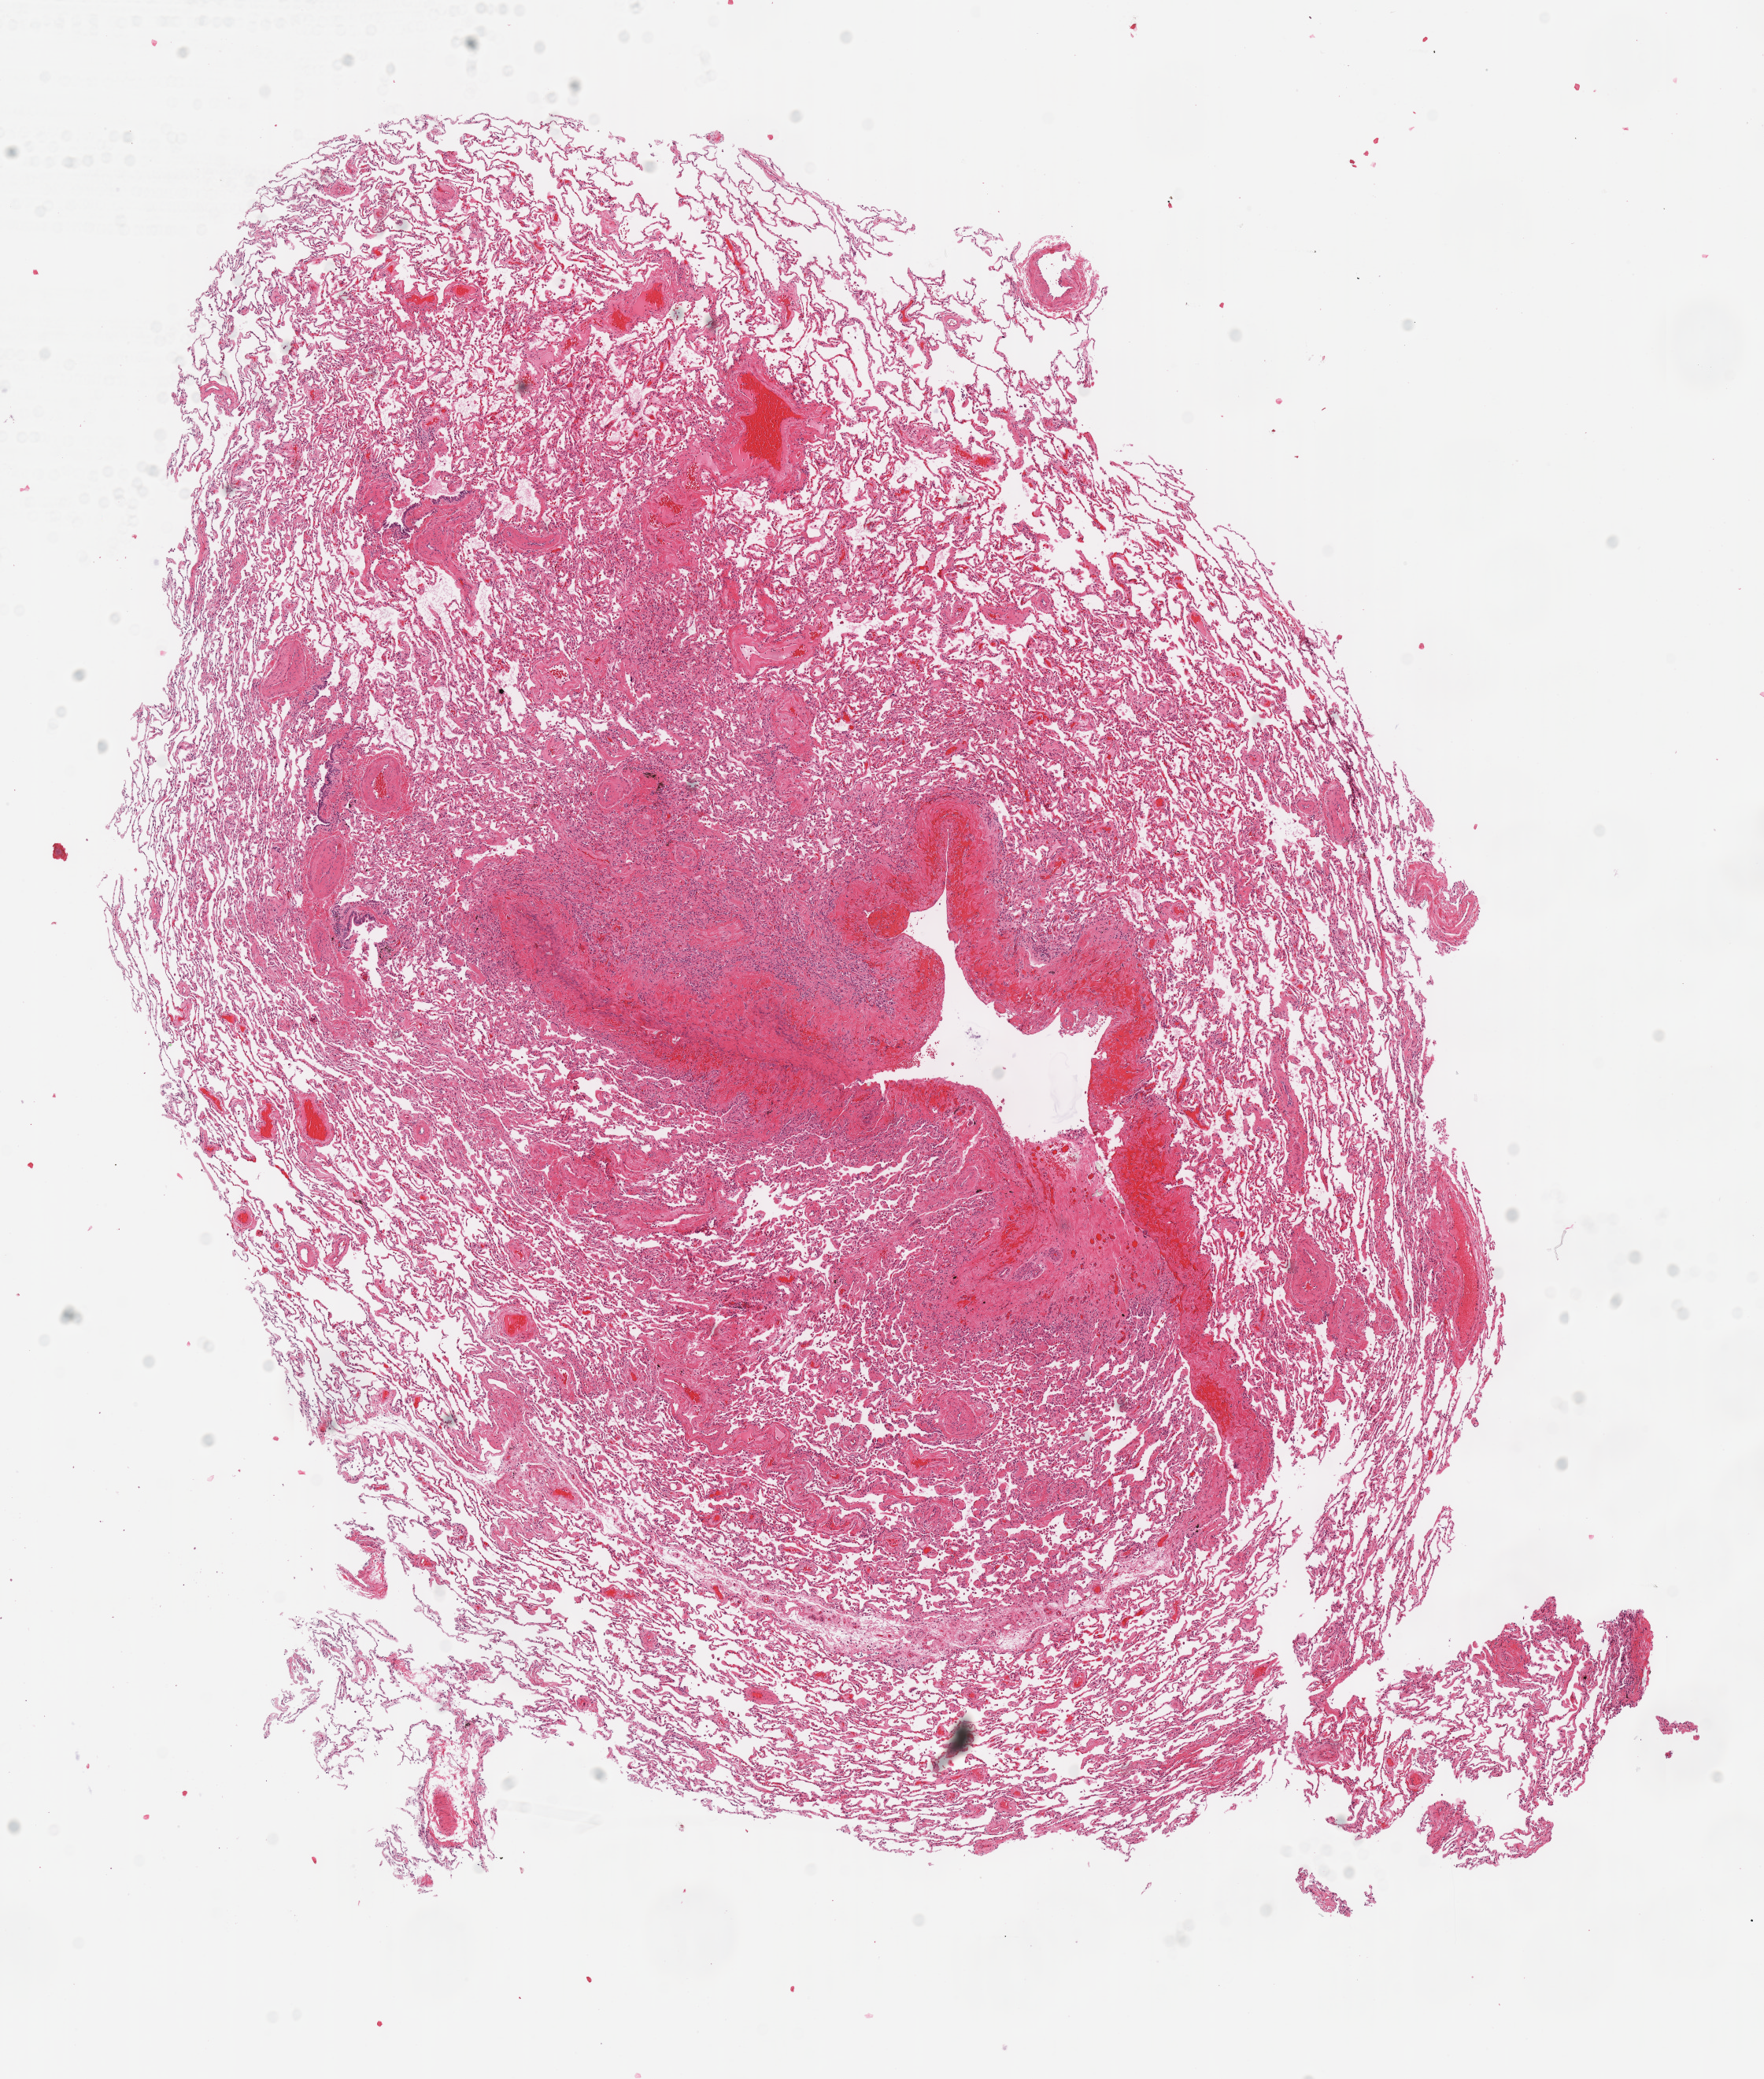
Hematoxylin and eosin (H&E) stained whole-slide image, shown as a low-resolution overview of the whole scanned area (about 8.8 x 10.4 mm), frozen section from the top of the tissue portion, lung, solid tissue normal (non-tumour tissue) sample. Patient: female, age at initial diagnosis 56 years.
This section: solid tissue normal sample (biorepository sample class). Patient diagnosis: Squamous cell carcinoma, NOS.